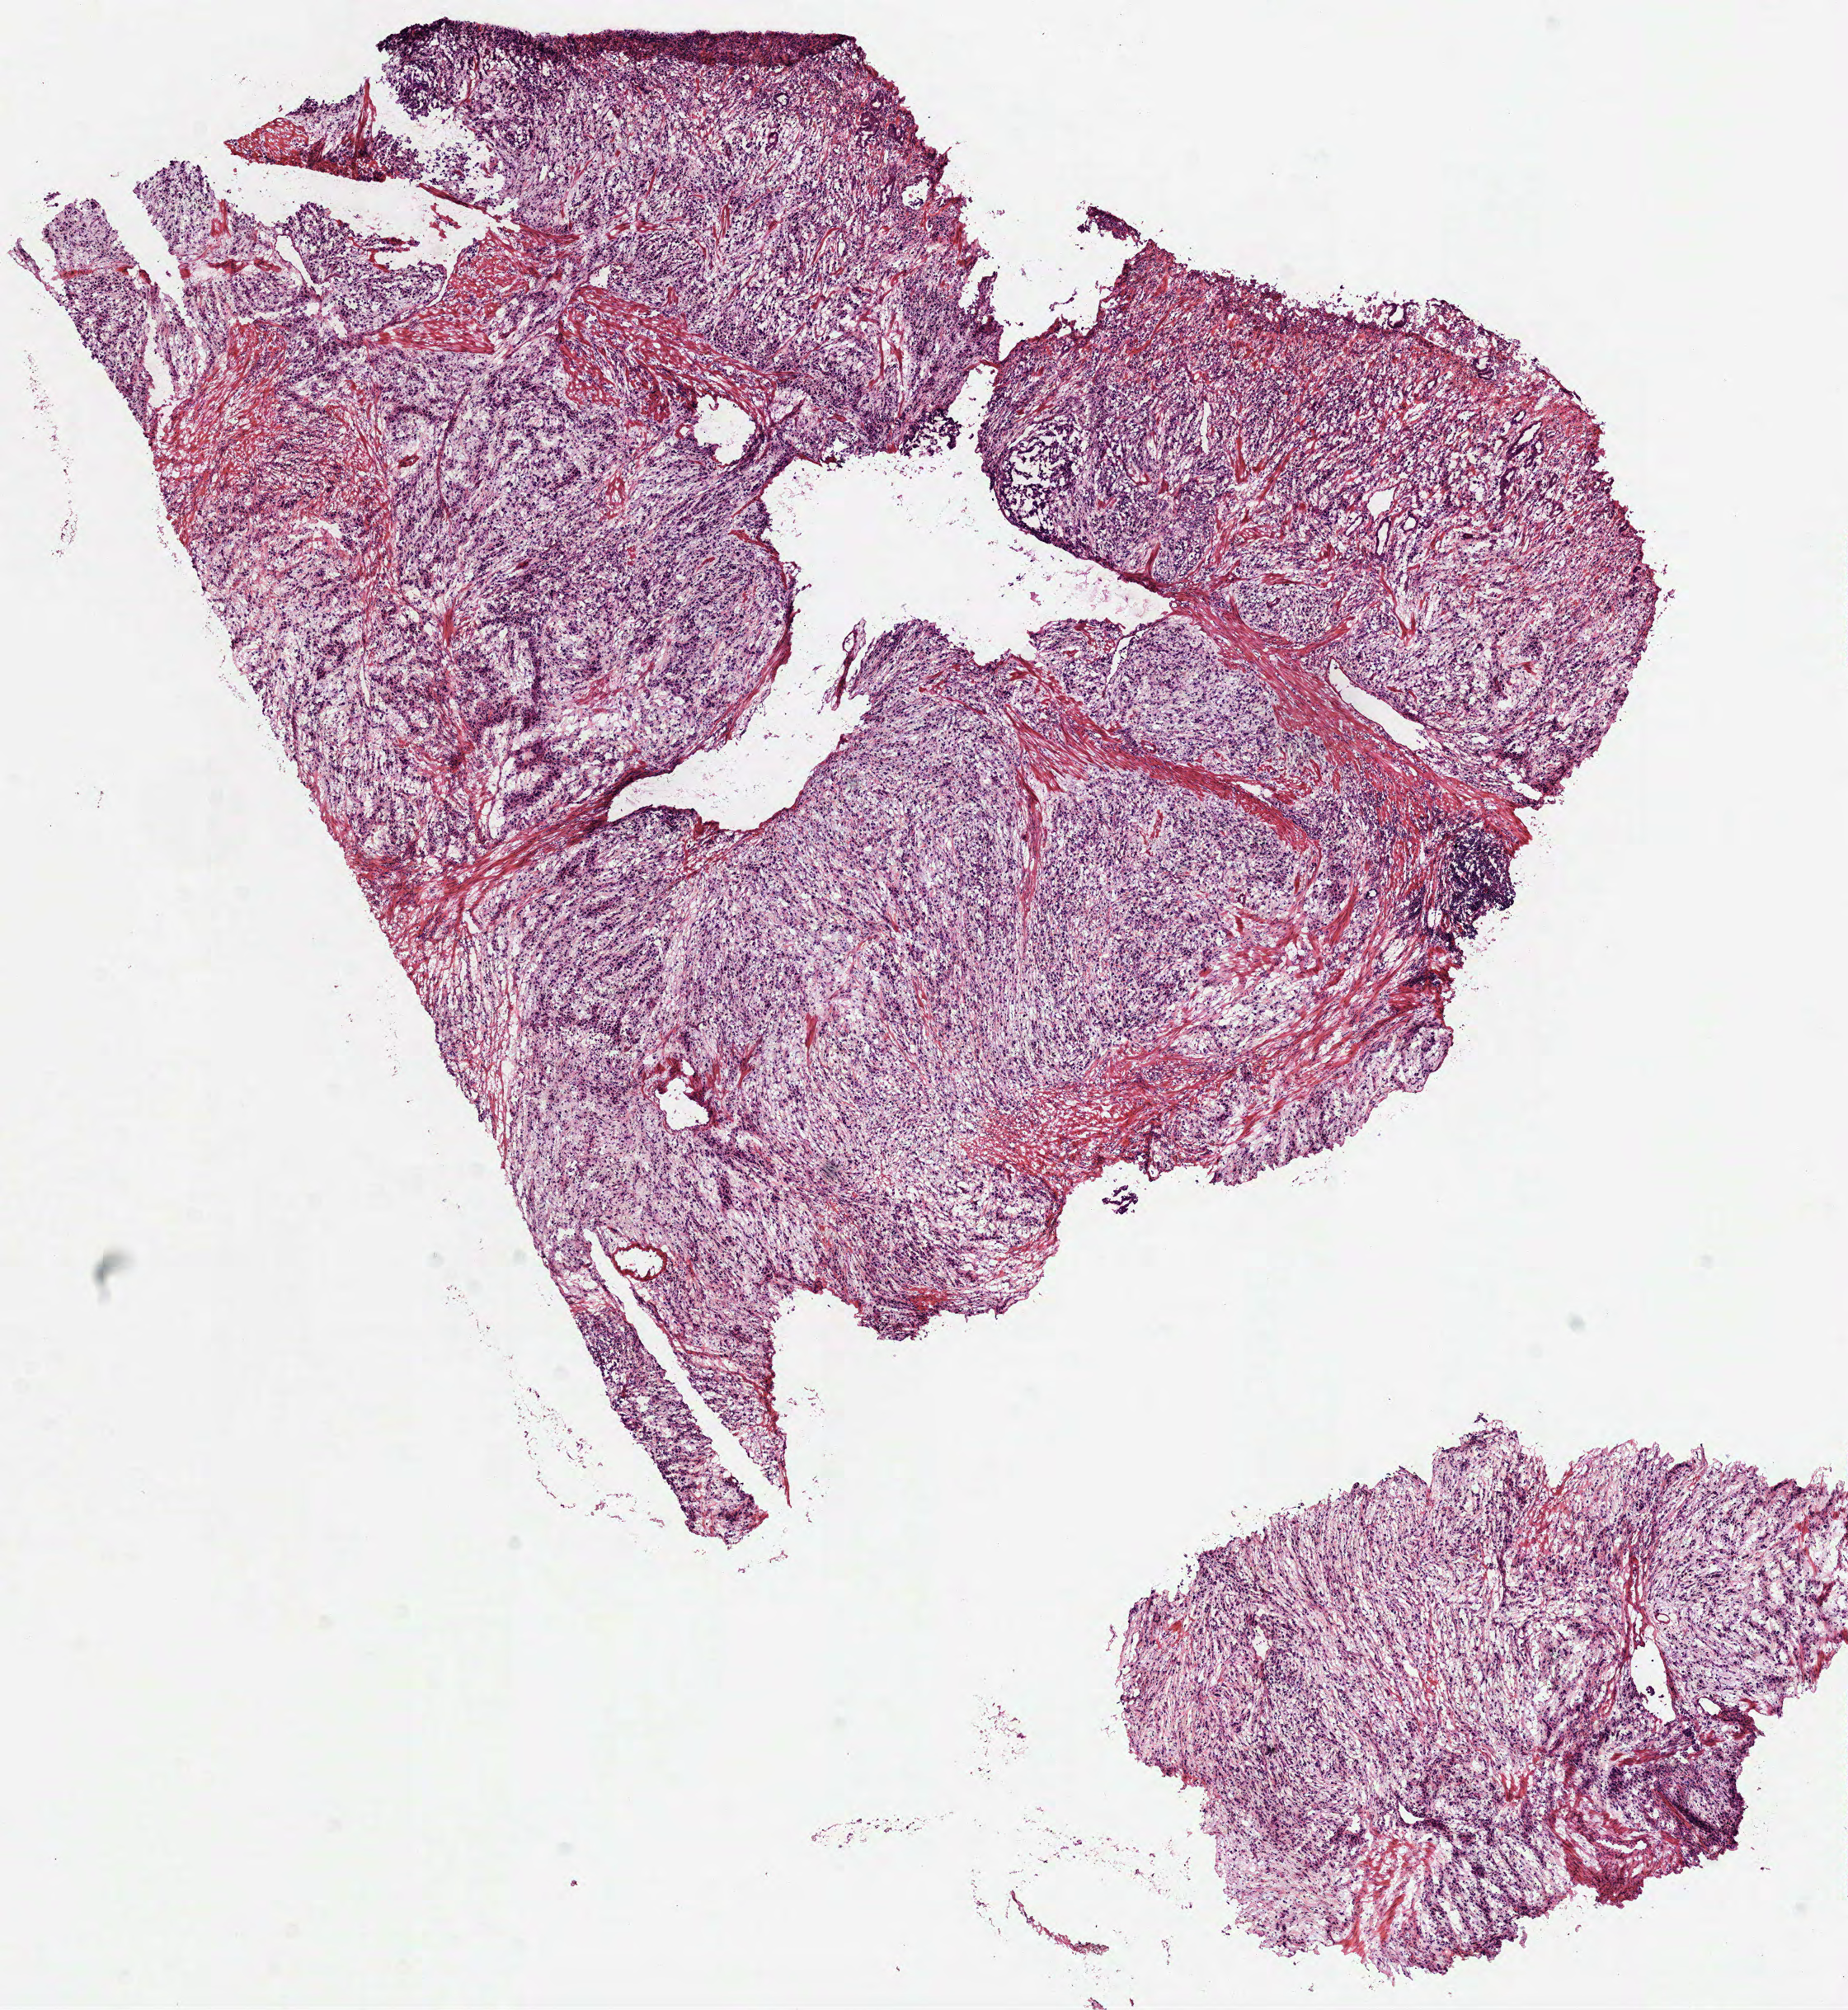
Digitized H&E-stained tissue section (whole slide) — whole scanned area (about 9.0 x 9.8 mm) shown as a low-resolution overview, frozen section, primary tumour sample from the stomach. Patient: male, age at initial diagnosis 51 years. Histologic grade: G3 (poorly differentiated). Slide review estimates, as recorded: tumour cells 90%, tumour nuclei 85%, normal cells 0%, stromal cells 10%, necrosis 0%.
- diagnosis: Carcinoma, diffuse type (fundus of stomach)
- AJCC pathologic stage: II (6th edition)
- TNM: T3 N0 M0